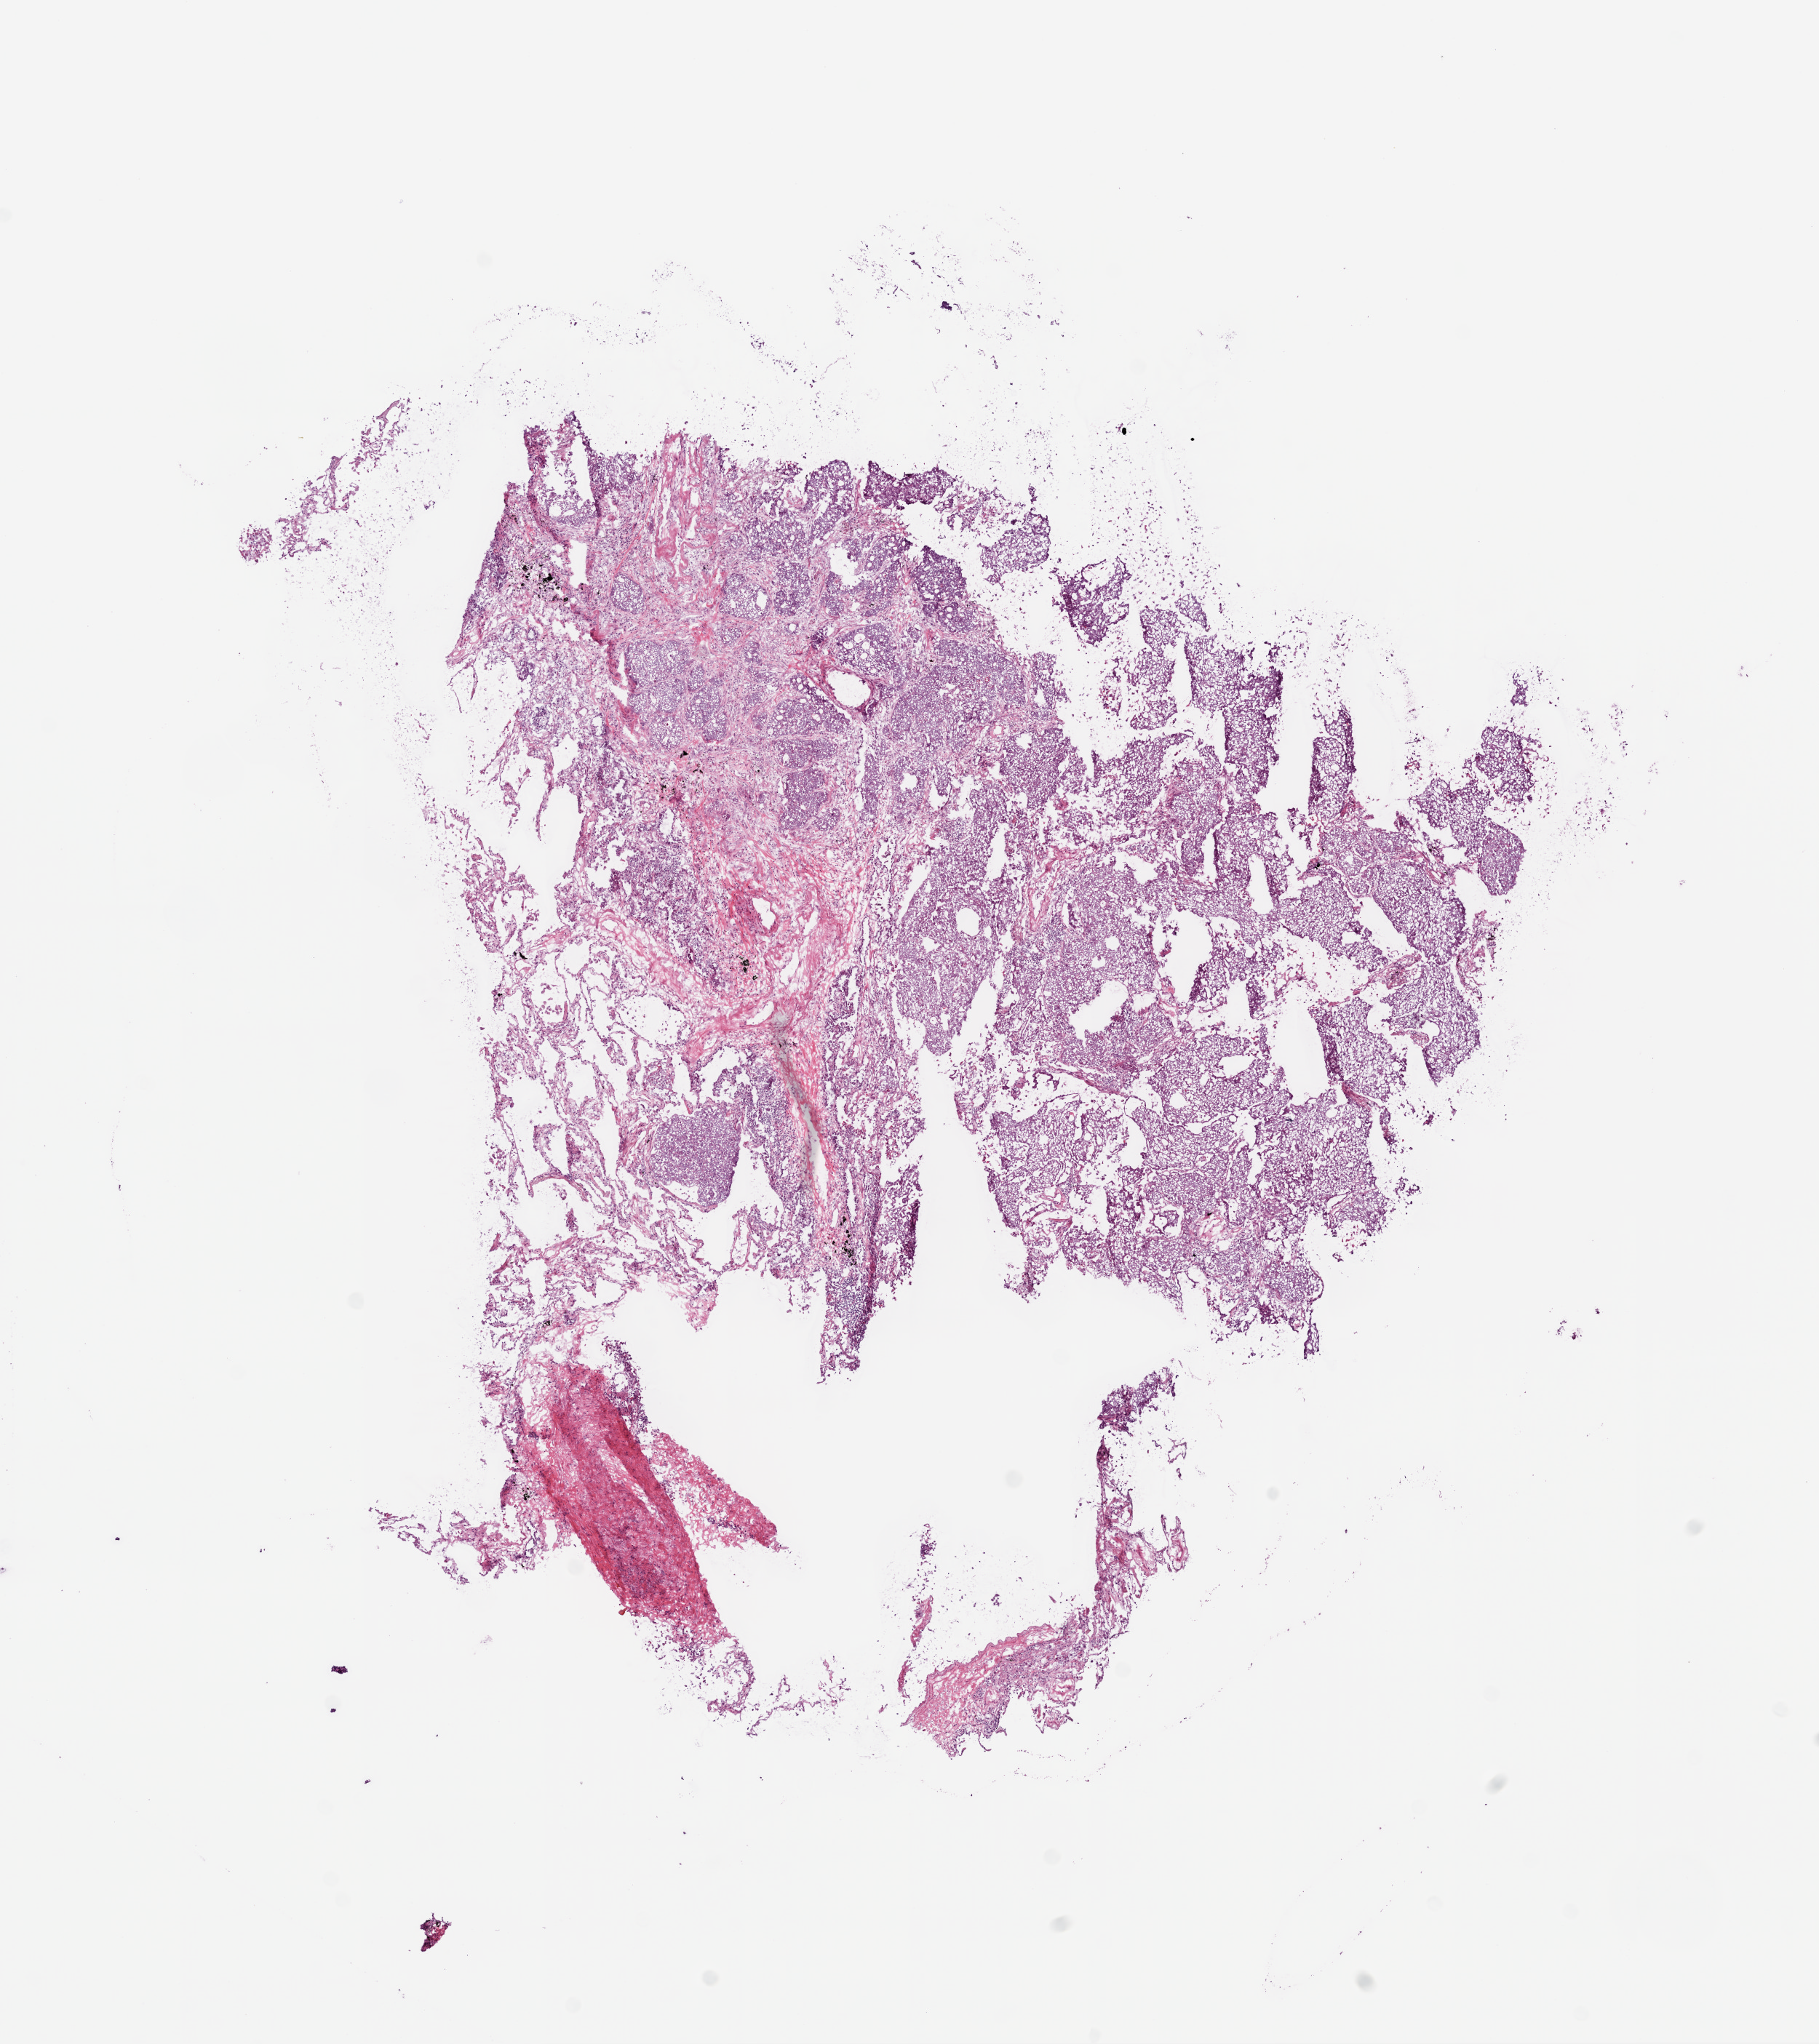
H&E-stained whole-slide image — a low-resolution overview of the entire scanned area, about 10.0 x 11.3 mm. Frozen section from the bottom of the tissue portion. Primary tumour sample from the lung. Male patient; age at initial diagnosis 74 years. Slide review estimates, as recorded: tumour cells 70%, tumour nuclei 80%, normal cells 15%, stromal cells 10%, necrosis 5%.
Histologic diagnosis: Adenocarcinoma, NOS (upper lobe, lung). AJCC pathologic stage: IIIA (6th edition).